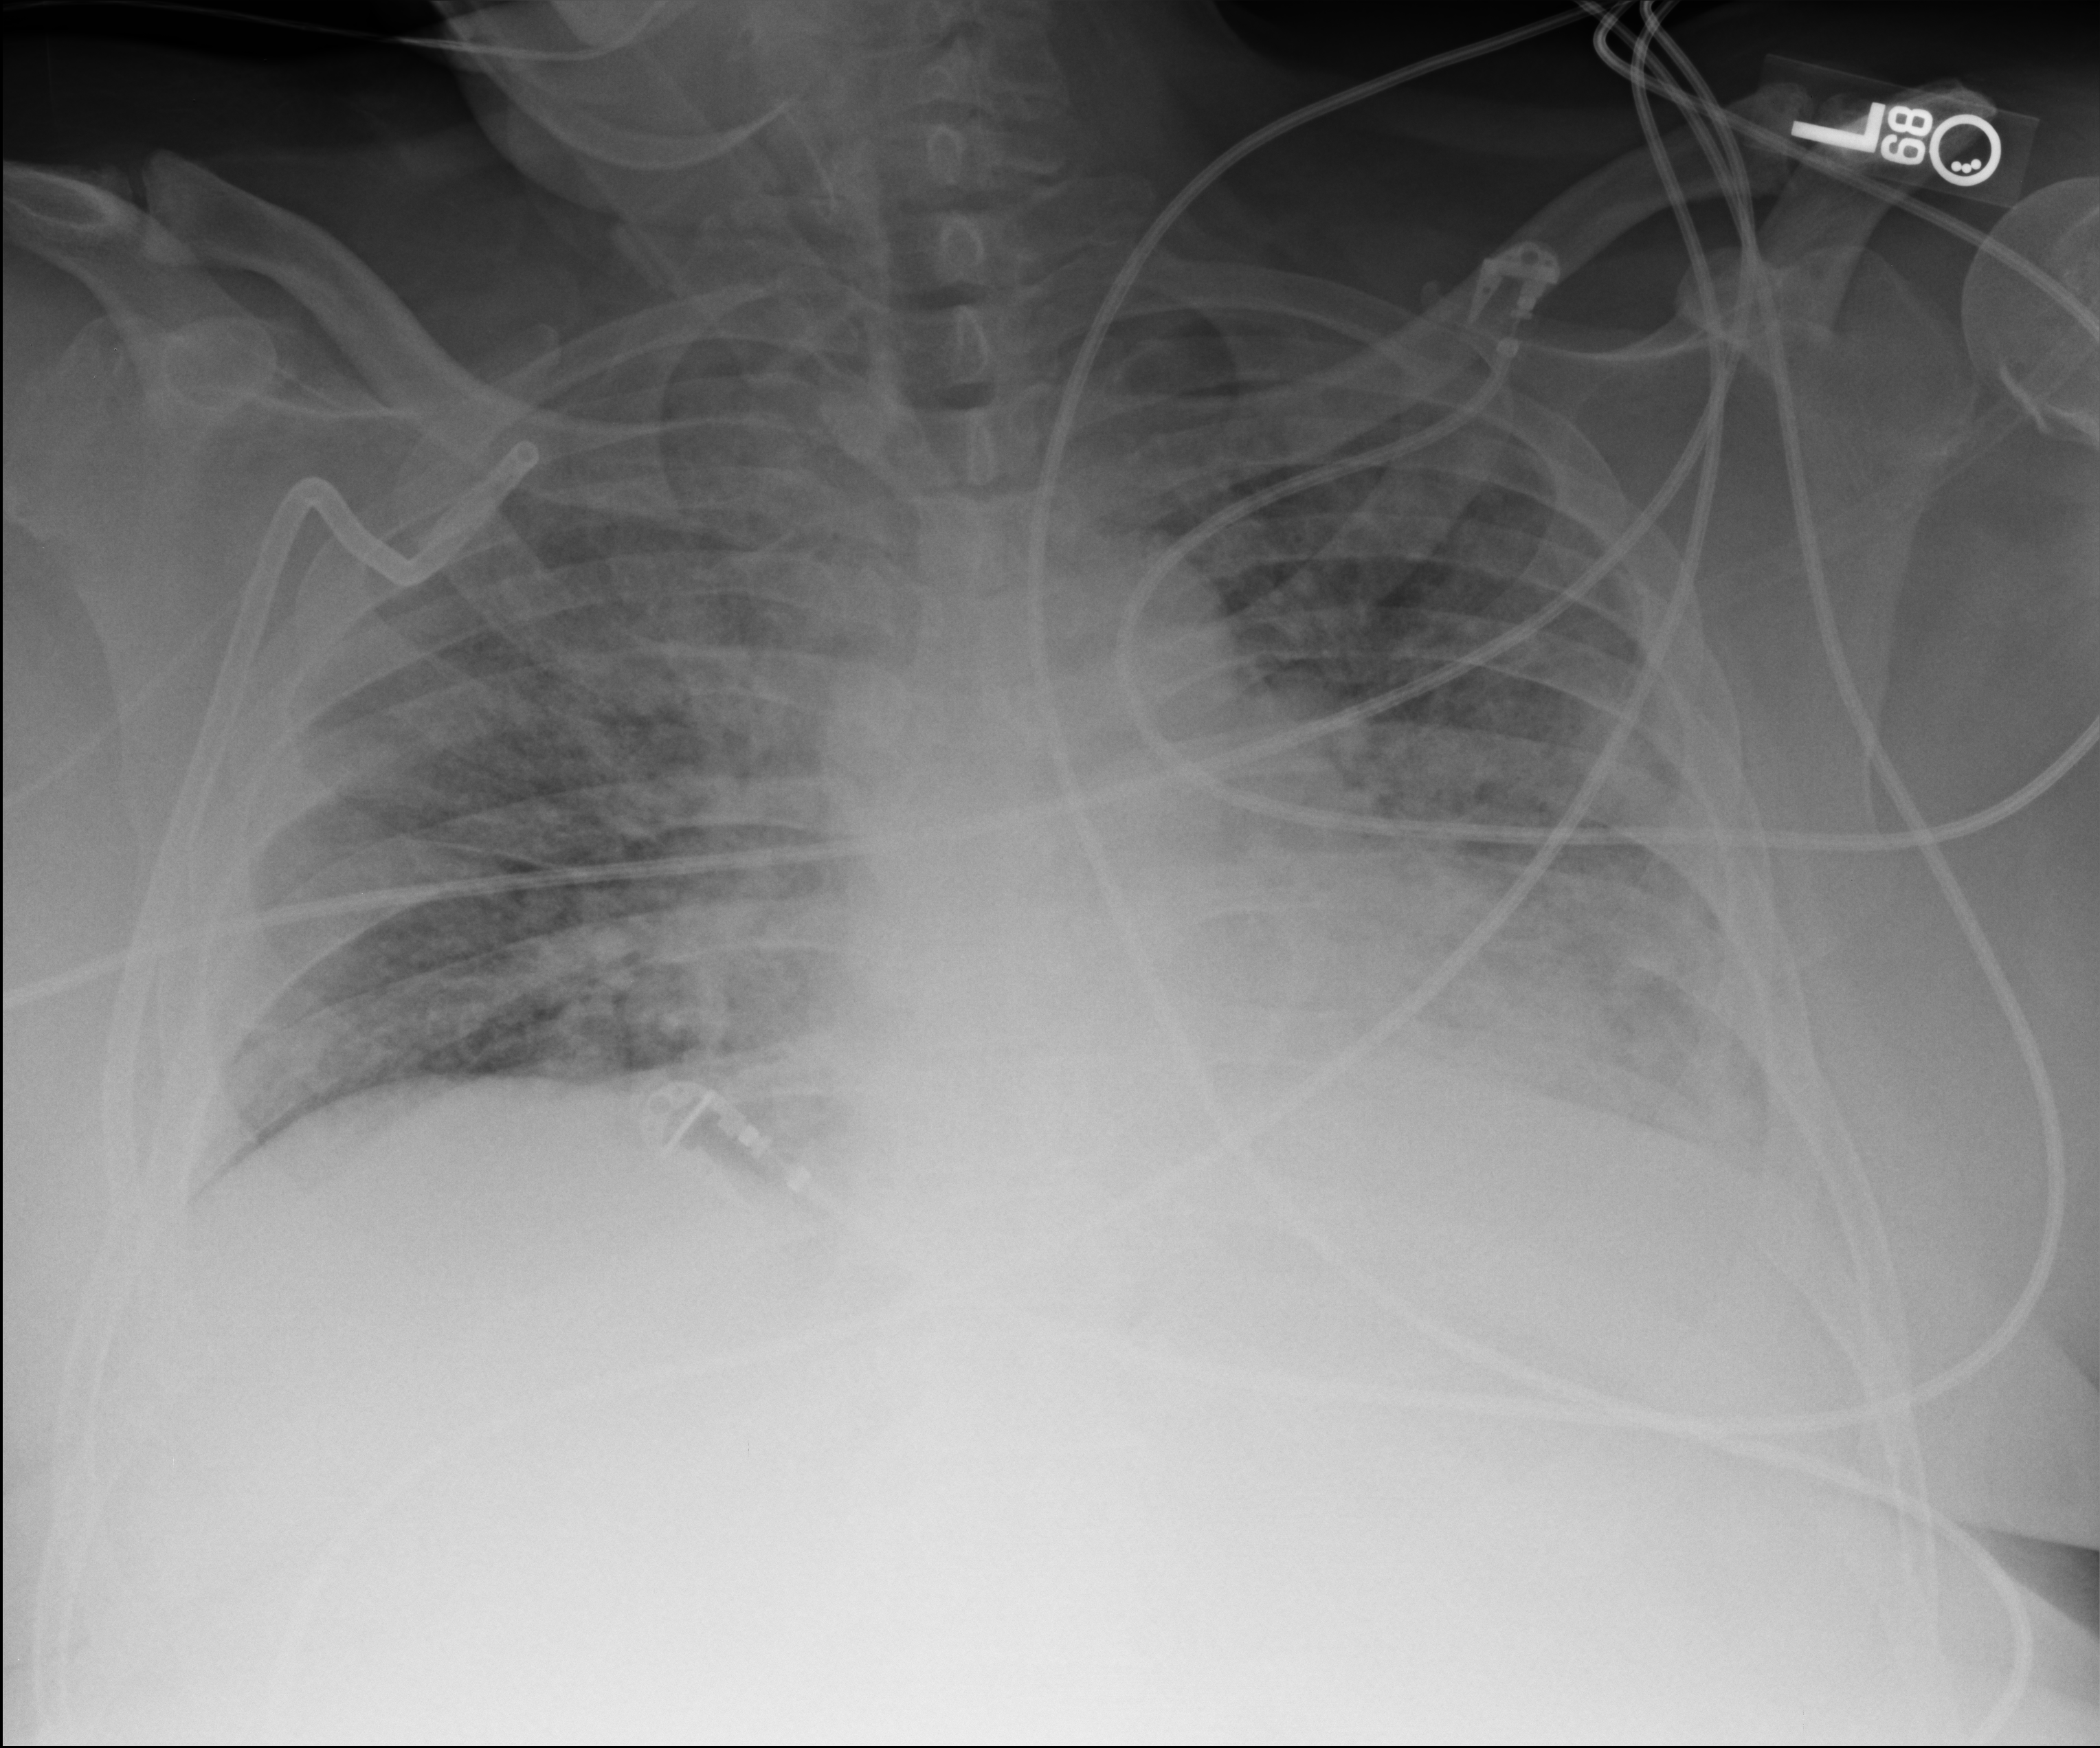
Portable chest radiograph; anteroposterior (AP) projection. Male patient hospitalised with COVID-19, age 60–74 years.
Hospital-stay facts (about this admission, not read from this image; timing relative to this image not recorded):
- admitted to intensive care during this hospital stay: yes
- mechanically ventilated during this hospital stay: yes
- hypertension (admission record): yes